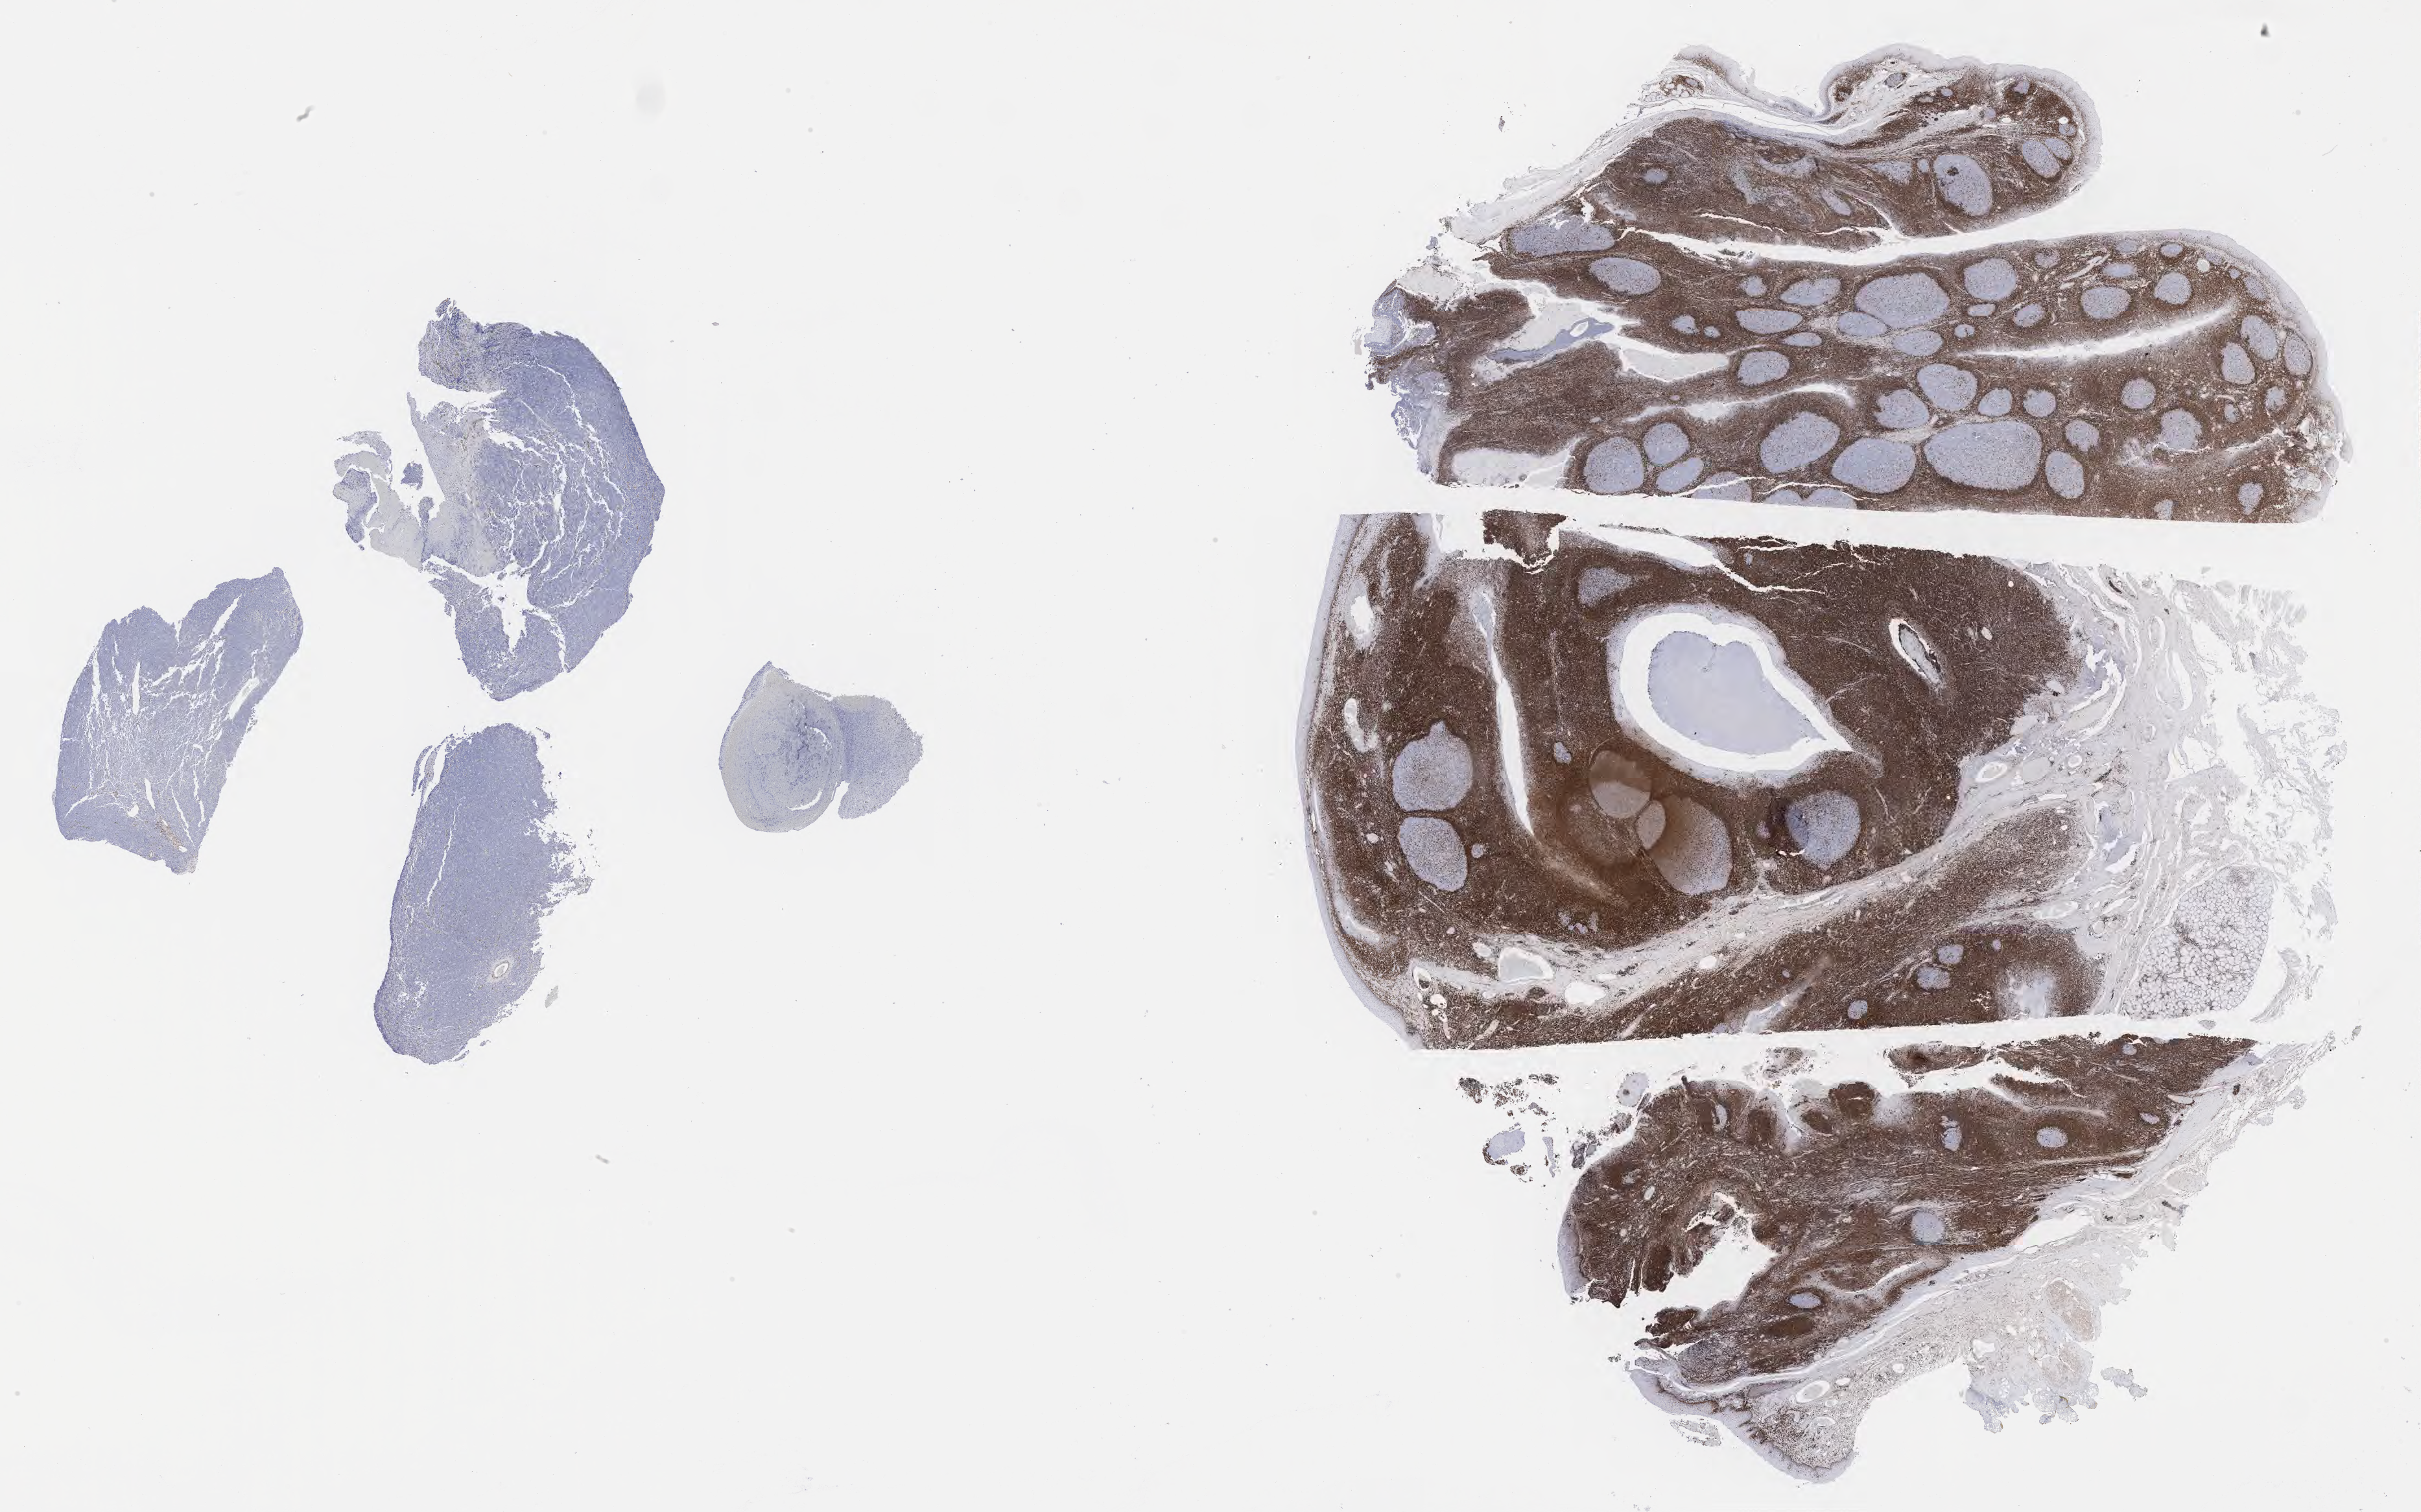
Immunohistochemistry (IHC) whole-slide image stained for BCL2, a low-resolution overview of the entire scanned area, about 30.2 x 18.9 mm, tumor tissue. Patient: male, 10 years old.
Histologic diagnosis: Burkitt lymphoma, NOS.